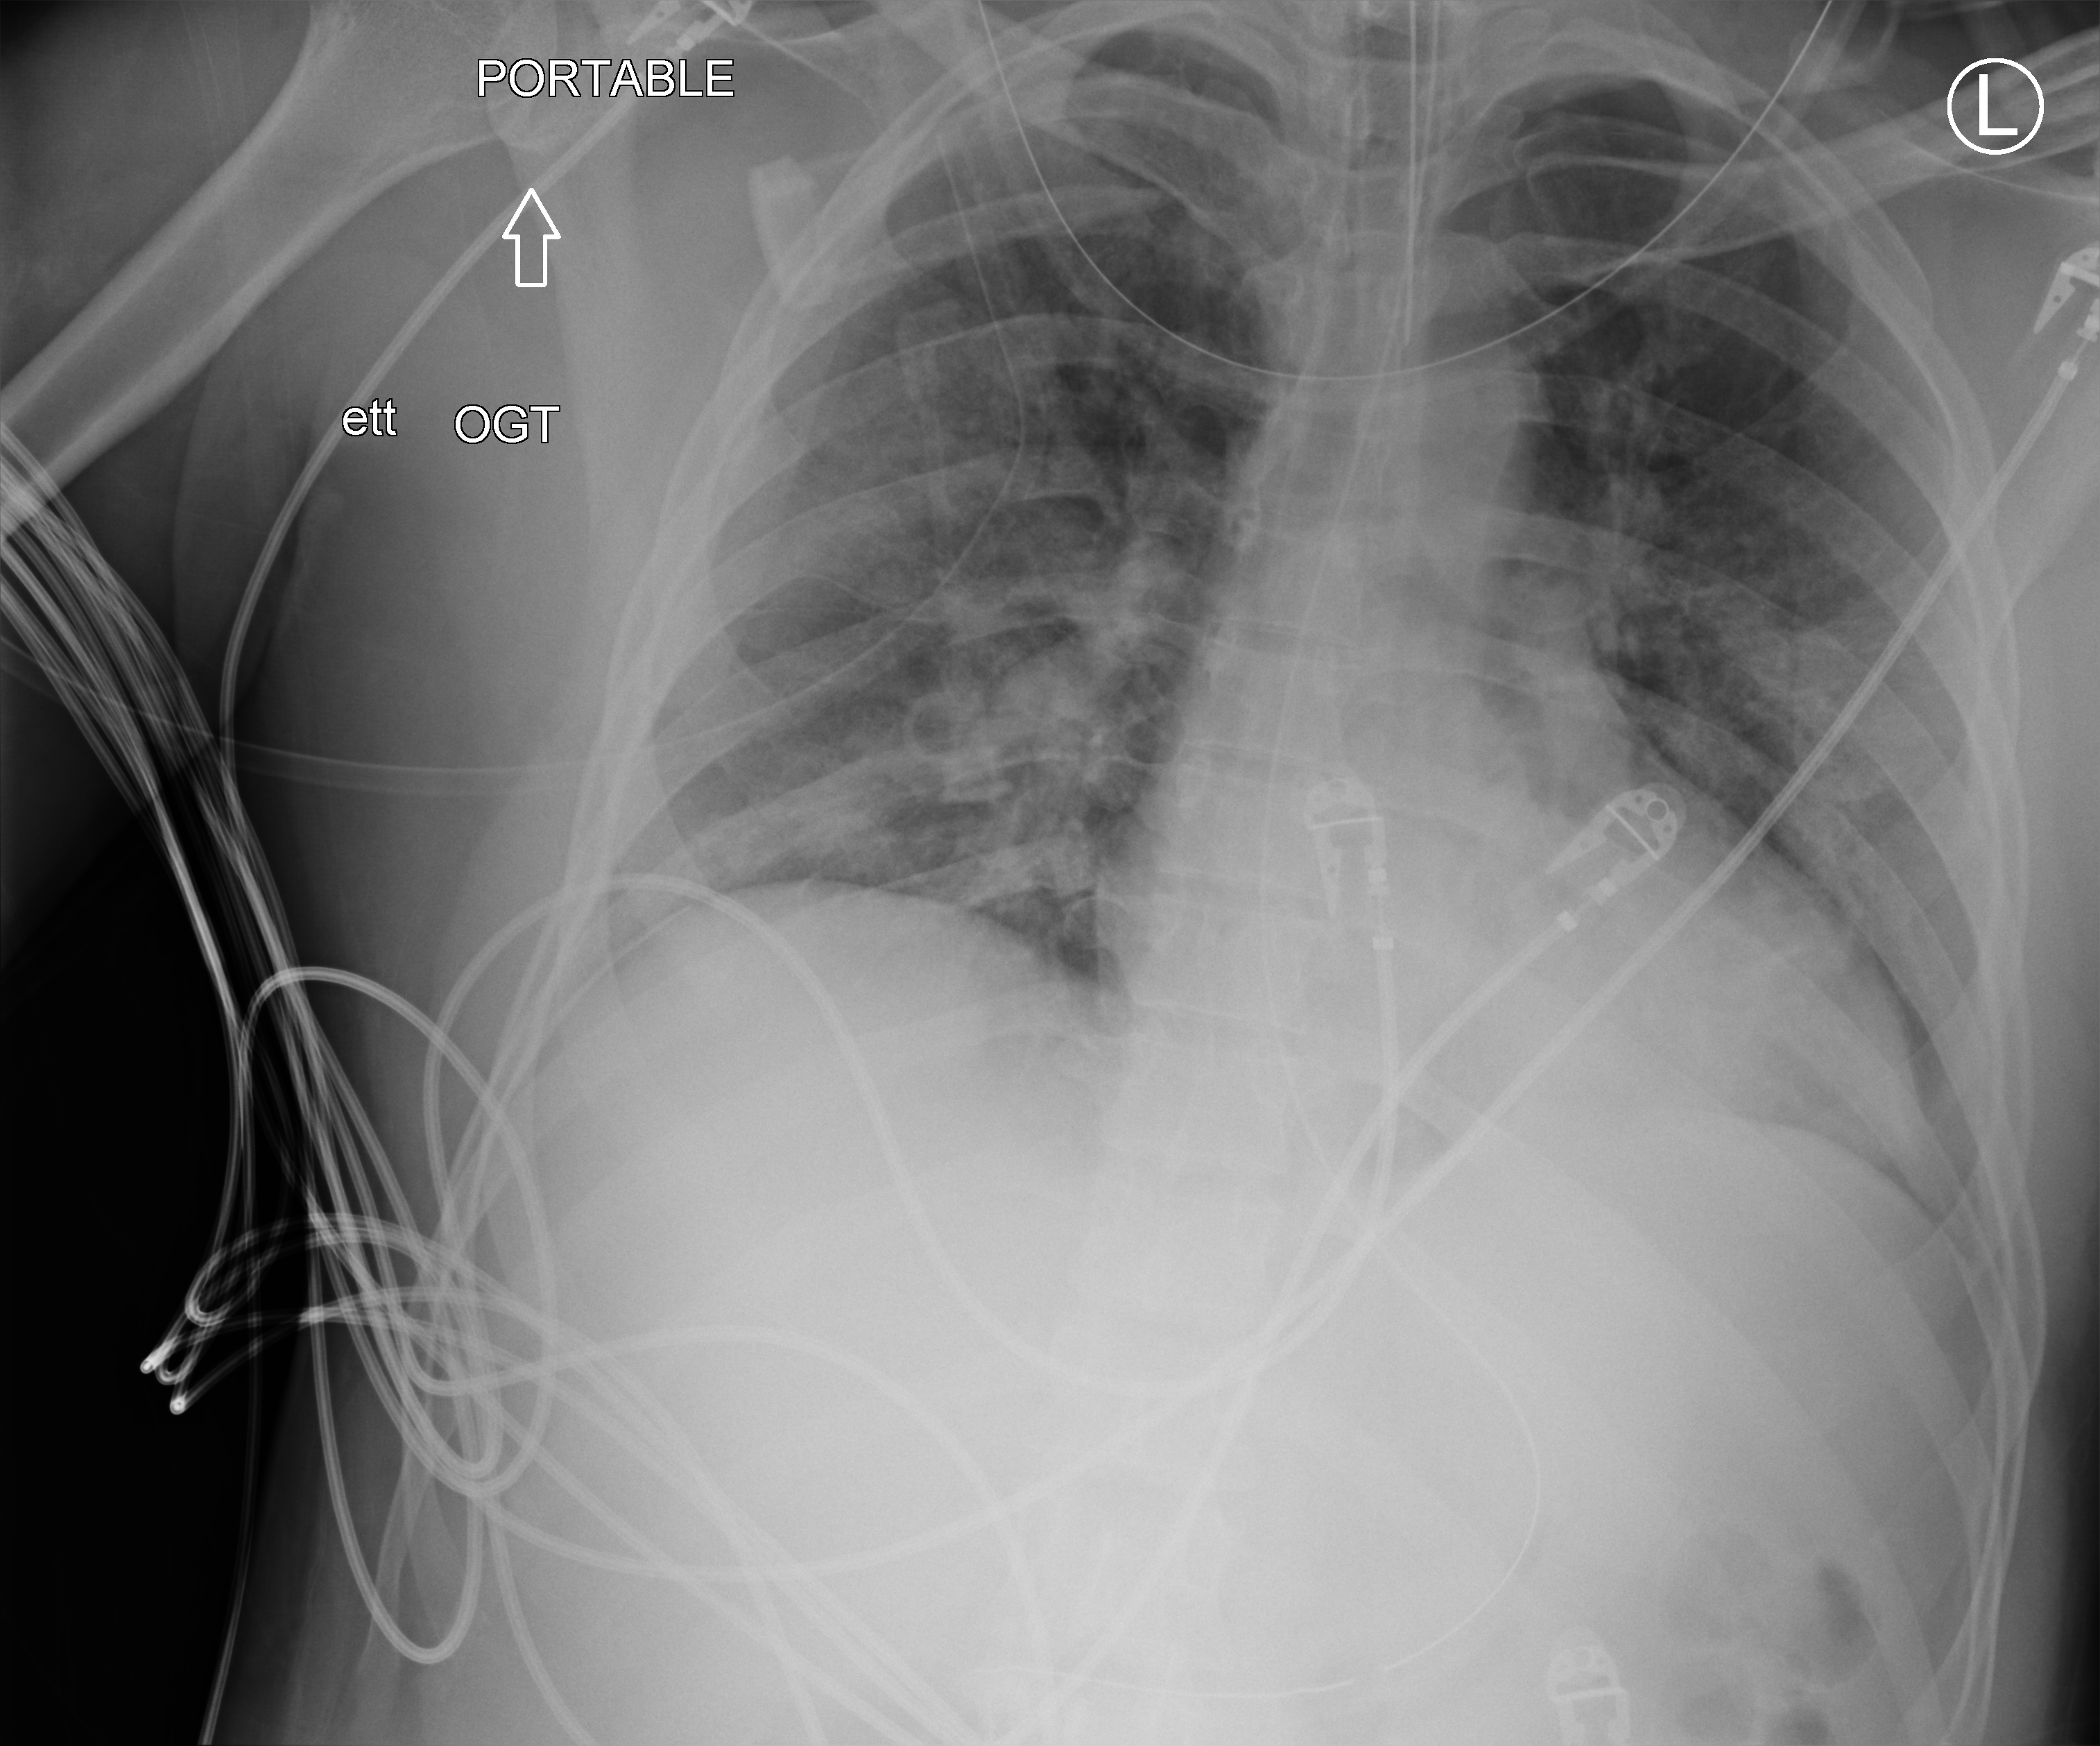
Chest X-ray (portable); anteroposterior (AP) projection. Male patient hospitalised with COVID-19, age 18–59 years.
Admission-level facts for this patient (not findings on this image; timing relative to this image not recorded):
- admitted to intensive care during this hospital stay: yes
- mechanically ventilated during this hospital stay: yes